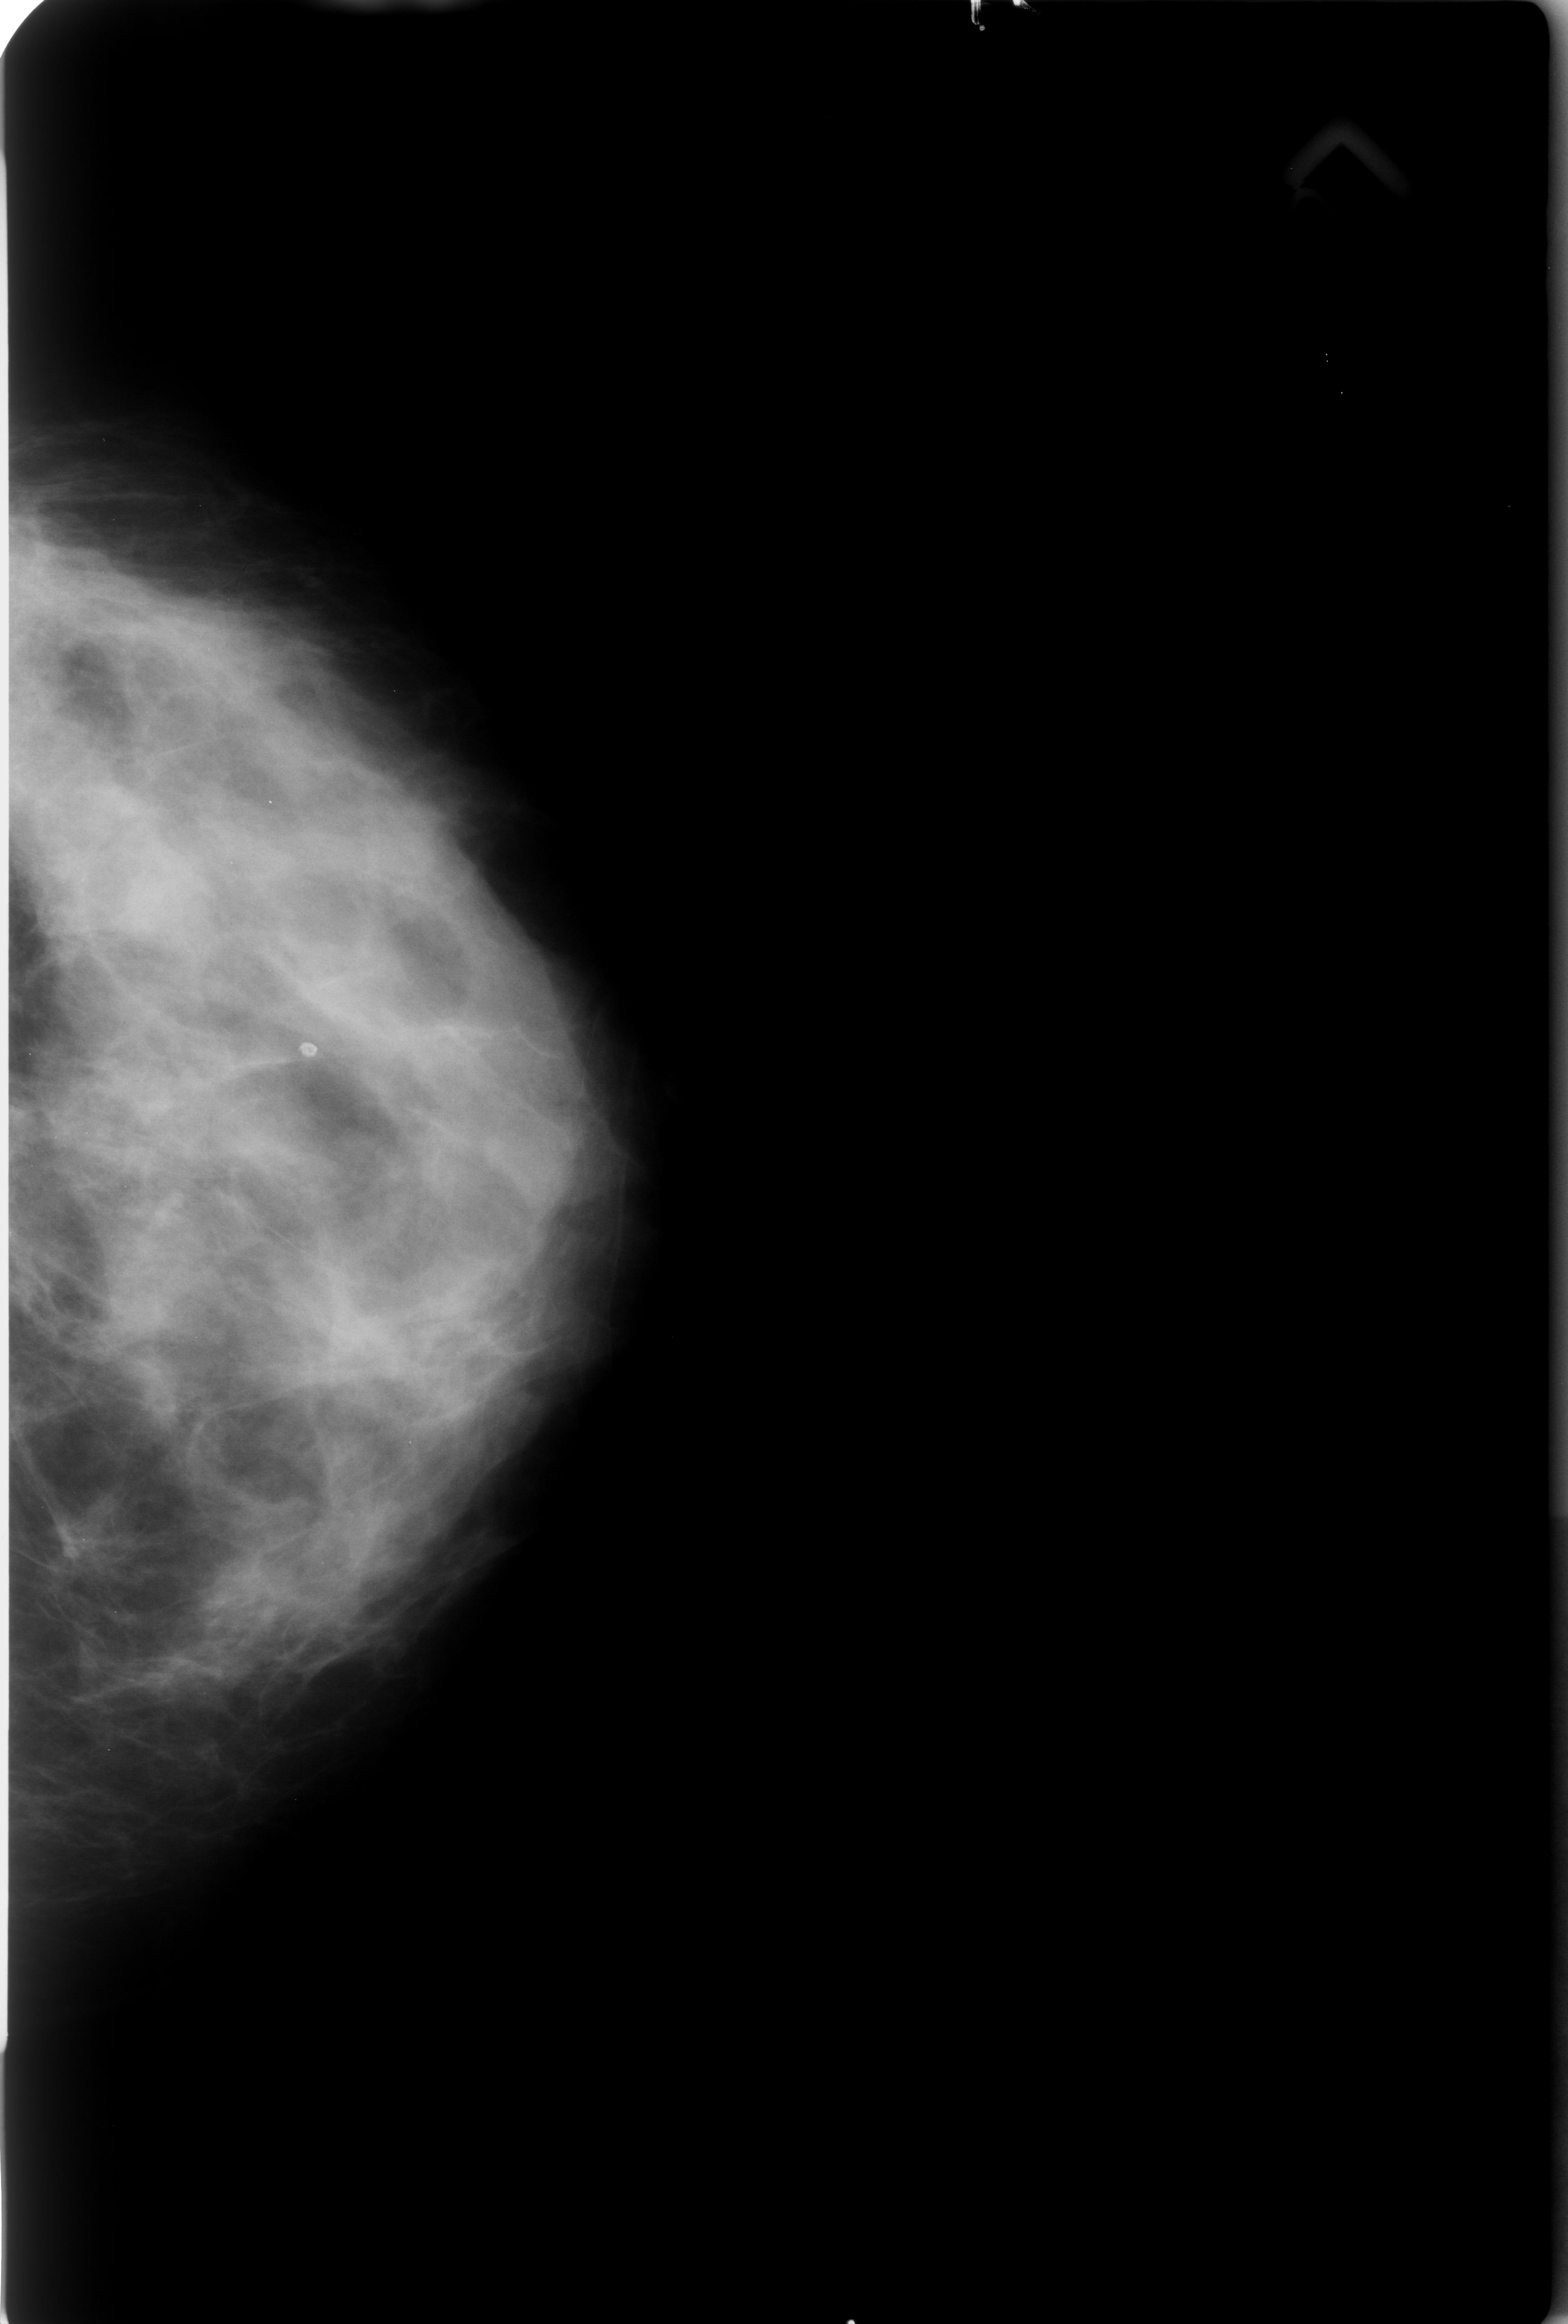
Scanned film-screen mammogram; left breast; CC view; BI-RADS breast density category 3 (scale 1–4); 1568 × 2324 image matrix.
Marked abnormalities (boxes around the expert regions of interest):
- calcifications, morphology lucent center; BI-RADS assessment category 2; subtlety rating 4 on a 1 (subtle) to 5 (obvious) scale; outcome (as recorded, no biopsy): benign without callback (not worked up further): bounding box [x1, y1, x2, y2] px = [296, 1036, 322, 1061]